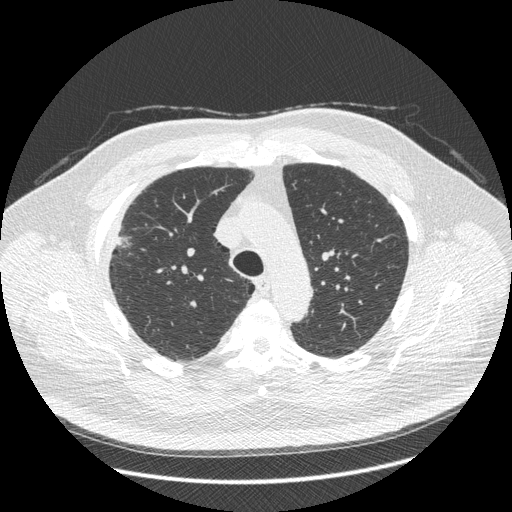
Chest CT (low-dose screening protocol), one axial image; third screening round (two years after baseline); lung window (W 1500 / L -600 HU); standard (soft-tissue) reconstruction kernel (STANDARD); slice 110 of 426 in the series. Male, age 66 years at enrolment.
Expert reader's lesion annotation, box from (x=88, y=213) to (x=148, y=272) px. The exam's reader record, not a measurement of the box and not confirmed to be the same lesion: non-calcified nodule or mass ≥4 mm, right upper lobe, 48 × 25 mm, spiculated (stellate) margins, soft tissue attenuation, pre-existing on the prior screen: no. Official screen result: positive, other.